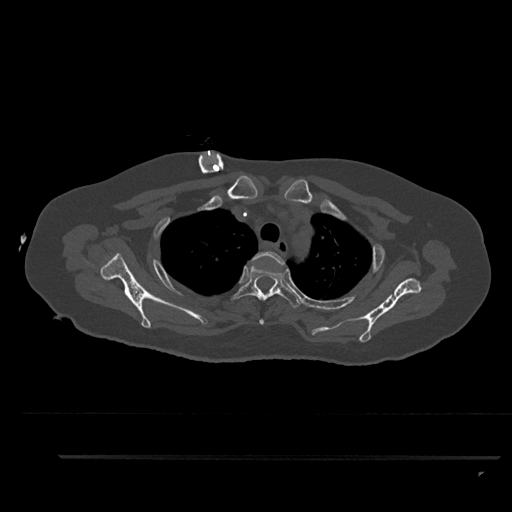
CT including the spine, one axial slice. Slice 694 of 797 in the series (ordered by position). Reconstruction kernel Br40s/3. 120 kVp. Bone window (W 1800 / L 400 HU). 512 × 512 image matrix, field of view 408 × 408 mm. Patient: female, 44 years. Case-level facts recorded for this patient, not image findings: primary cancer: renal.
Annotated regions visible in this slice (semi-automatically segmented with operator editing):
- T2 vertebra: bounding box (x1, y1, x2, y2) in pixels: (251, 251, 285, 325)
- T3 vertebra: (231, 266, 303, 308)